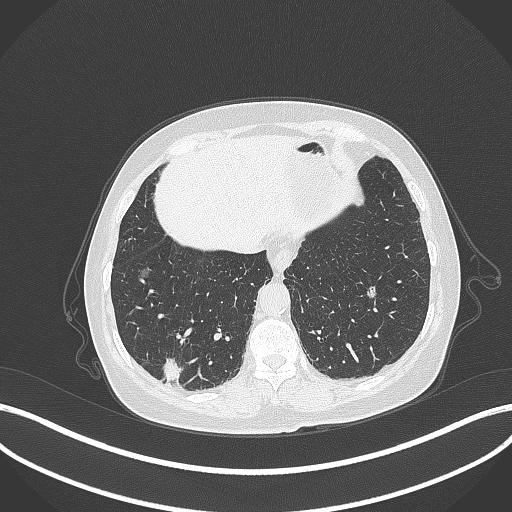
Chest CT, one axial slice. Slice 65 of 333 in the series (ordered by position). Reconstruction kernel B70f. Lung window (W 1500 / L -600 HU). 1 mm slice thickness. 512 × 512 image matrix, field of view 400 × 400 mm. Patient: female, 69 years. Case-level facts recorded for this patient, not image findings: clinical TNM (as recorded): T1b N0 M0; histopathological grade: G2-3.
Outlined on this slice (rectangle marked by the reading radiologist):
- lung tumour (recorded histology: adenocarcinoma): bounding box [x1, y1, x2, y2] px = [158, 354, 187, 386]